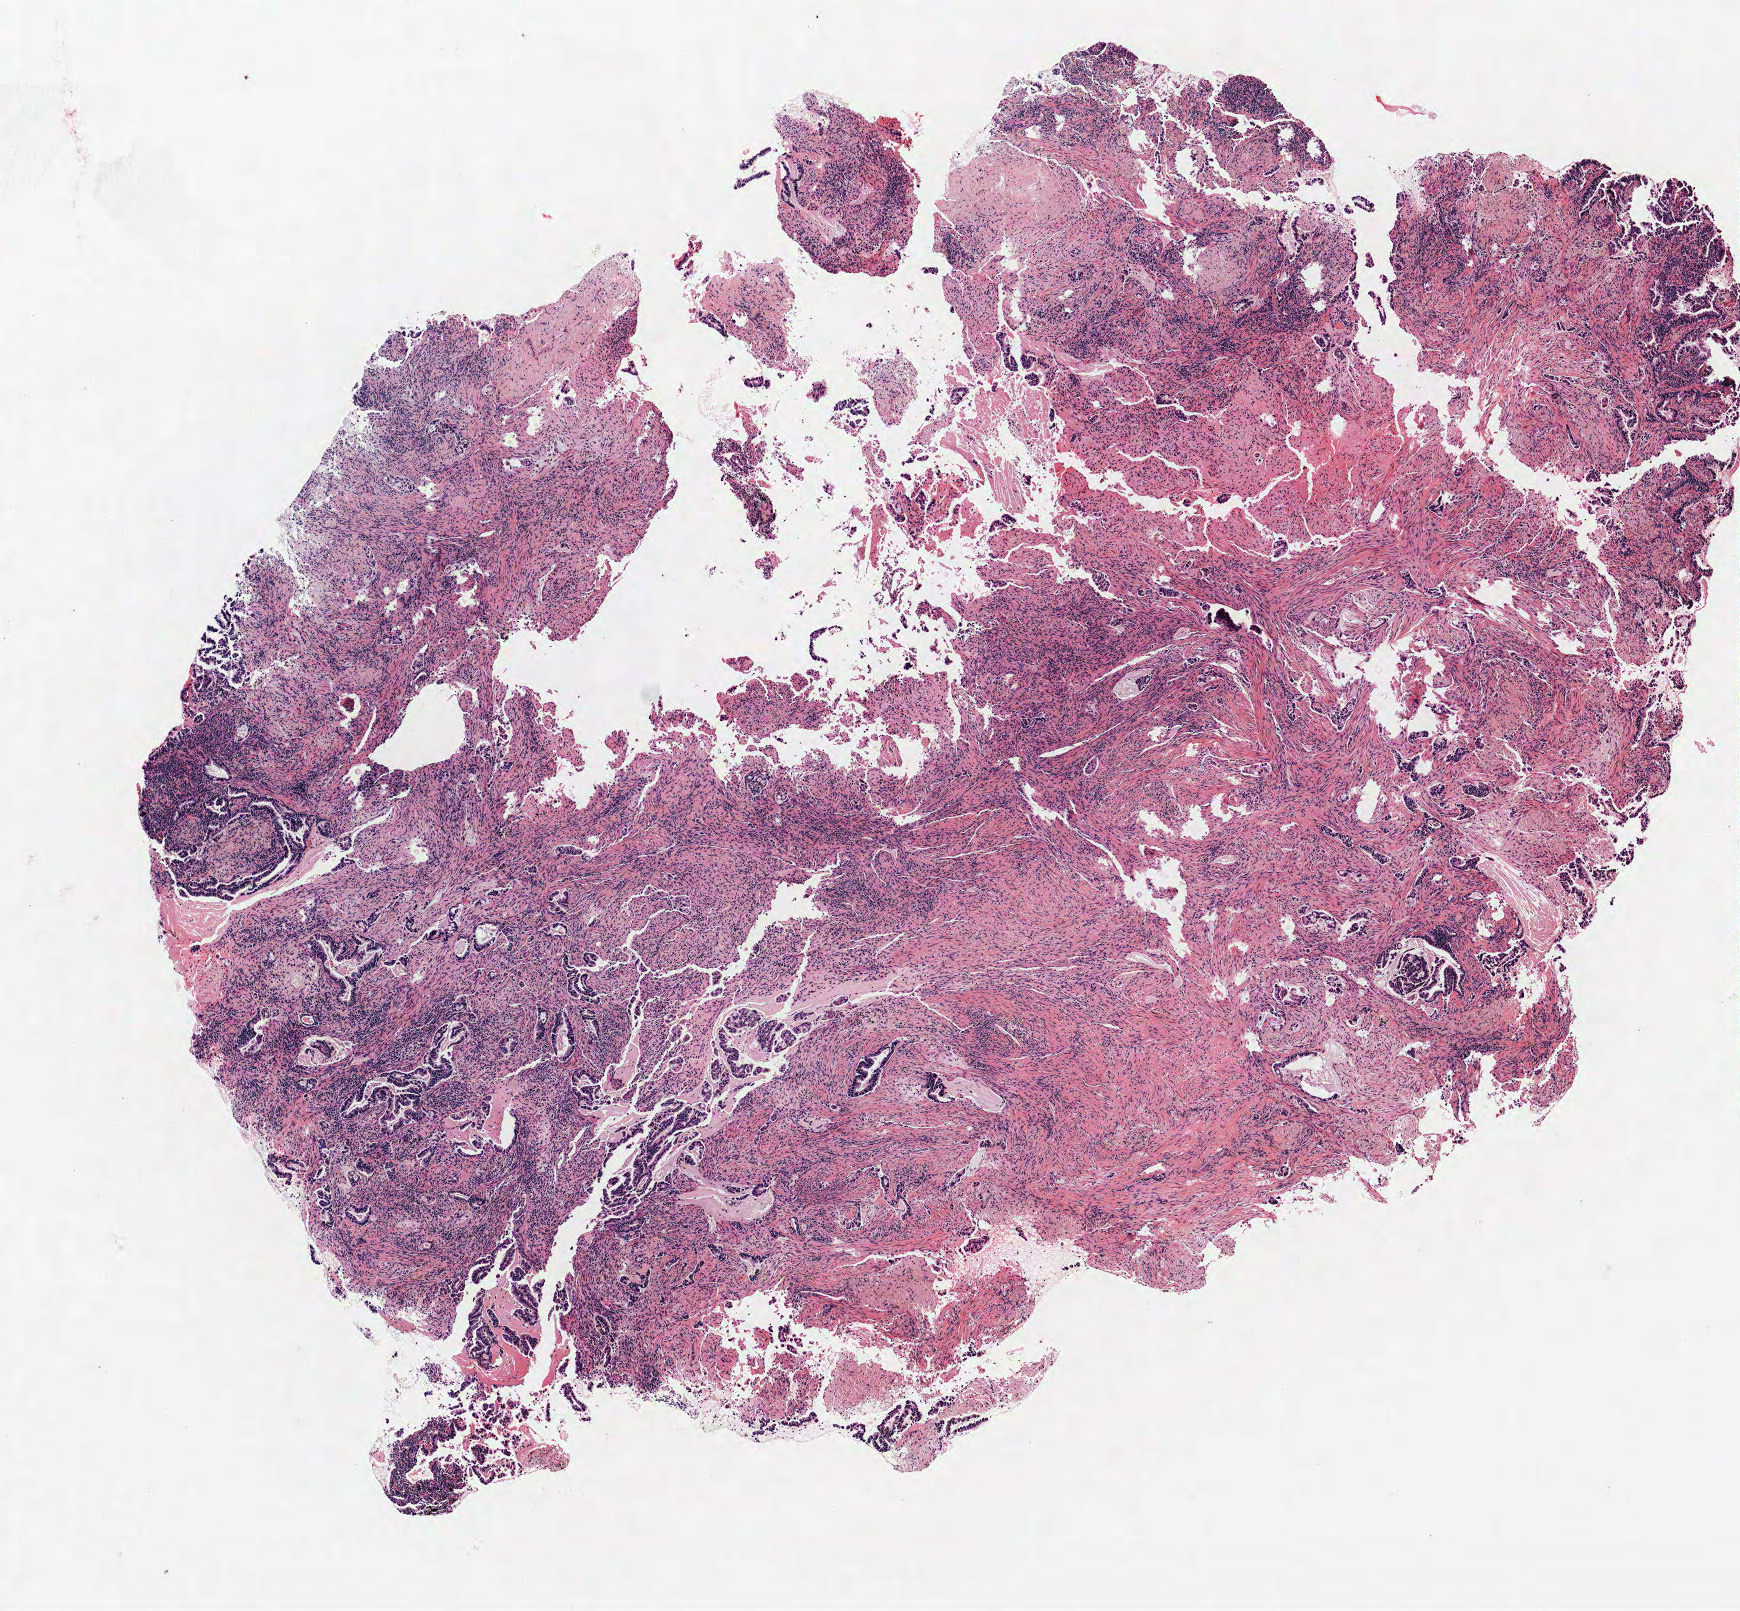
H&E-stained whole-slide image, whole scanned area (about 7.0 x 6.4 mm) shown as a low-resolution overview, formalin-fixed paraffin-embedded (FFPE) section, lung. Female patient, aged 62 at enrolment. Current smoker at enrolment.
Participant's lung-cancer diagnosis: Adenocarcinoma, NOS.